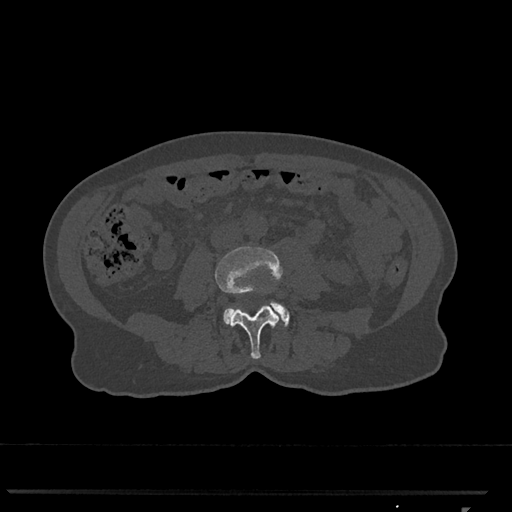
CT including the spine, one axial slice. Position 251 of 793 along the scan axis. Reconstruction kernel Br40s/3. 120 kVp. Bone window (W 1800 / L 400 HU). 0.5 mm slice thickness. 512 × 512 image matrix, field of view 380 × 380 mm. Patient: female, 62 years. From the clinical record (not read from this slice): primary cancer: renal.
Structures marked on this image (semi-automatic segmentation, software-assisted and operator-edited):
- L3 vertebra: bounding box [x1, y1, x2, y2] px = [215, 246, 283, 359]
- L4 vertebra: [223, 301, 290, 327]